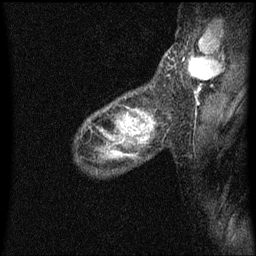
Breast MRI (dynamic contrast-enhanced), one sagittal slice; slice 45 of 60 in the series (ordered by position); dynamic contrast-enhanced series, image 2 of 3 at this slice position (ordered by acquisition); 1.5 T; TE 4.2 ms, TR 8.4 ms; 2 mm slice thickness; 256 × 256 image matrix, field of view 200 × 200 mm. Female patient, age 49 years.
Structures marked on this image (semi-automatically segmented with operator editing):
- analysis volume of interest (the breast-tissue region the enhancement analysis was run in; not a lesion): bounding box <103,98,157,151> (left, top, right, bottom; pixels)
- tumour enhancement mask (voxels above the 70 % enhancement threshold inside the analysis volume of interest): <127,114,131,127>